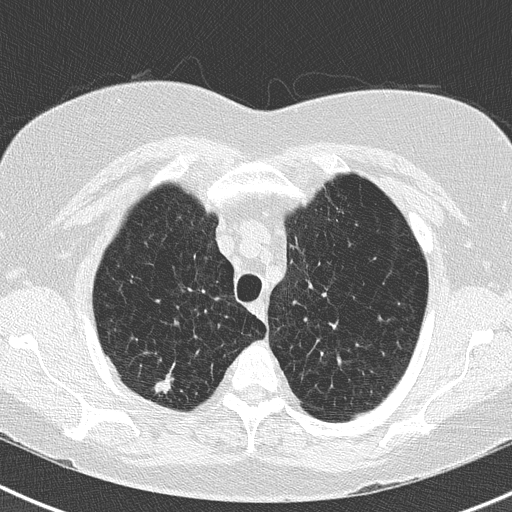
Low-dose screening chest CT, axial slice. Second annual screen. Lung window (W 1500 / L -600 HU). Slice 41 of 183 in the series. 512 × 512 image matrix, field of view 310 × 310 mm. Female, age 73 years at enrolment. Former smoker at enrolment.
• Expert reader's lesion annotation, box from (x=137, y=359) to (x=190, y=403) px.
• The screening reader recorded 2 non-calcified nodules or masses ≥4 mm on this exam (right upper lobe, right upper lobe); which of them this box marks is not recorded.
• Later outcome: lung cancer diagnosed 250 days after this screen — adenocarcinoma, NOS, right upper lobe, moderately differentiated (G2), stage IB (AJCC 6th edition), 15 mm at pathology.